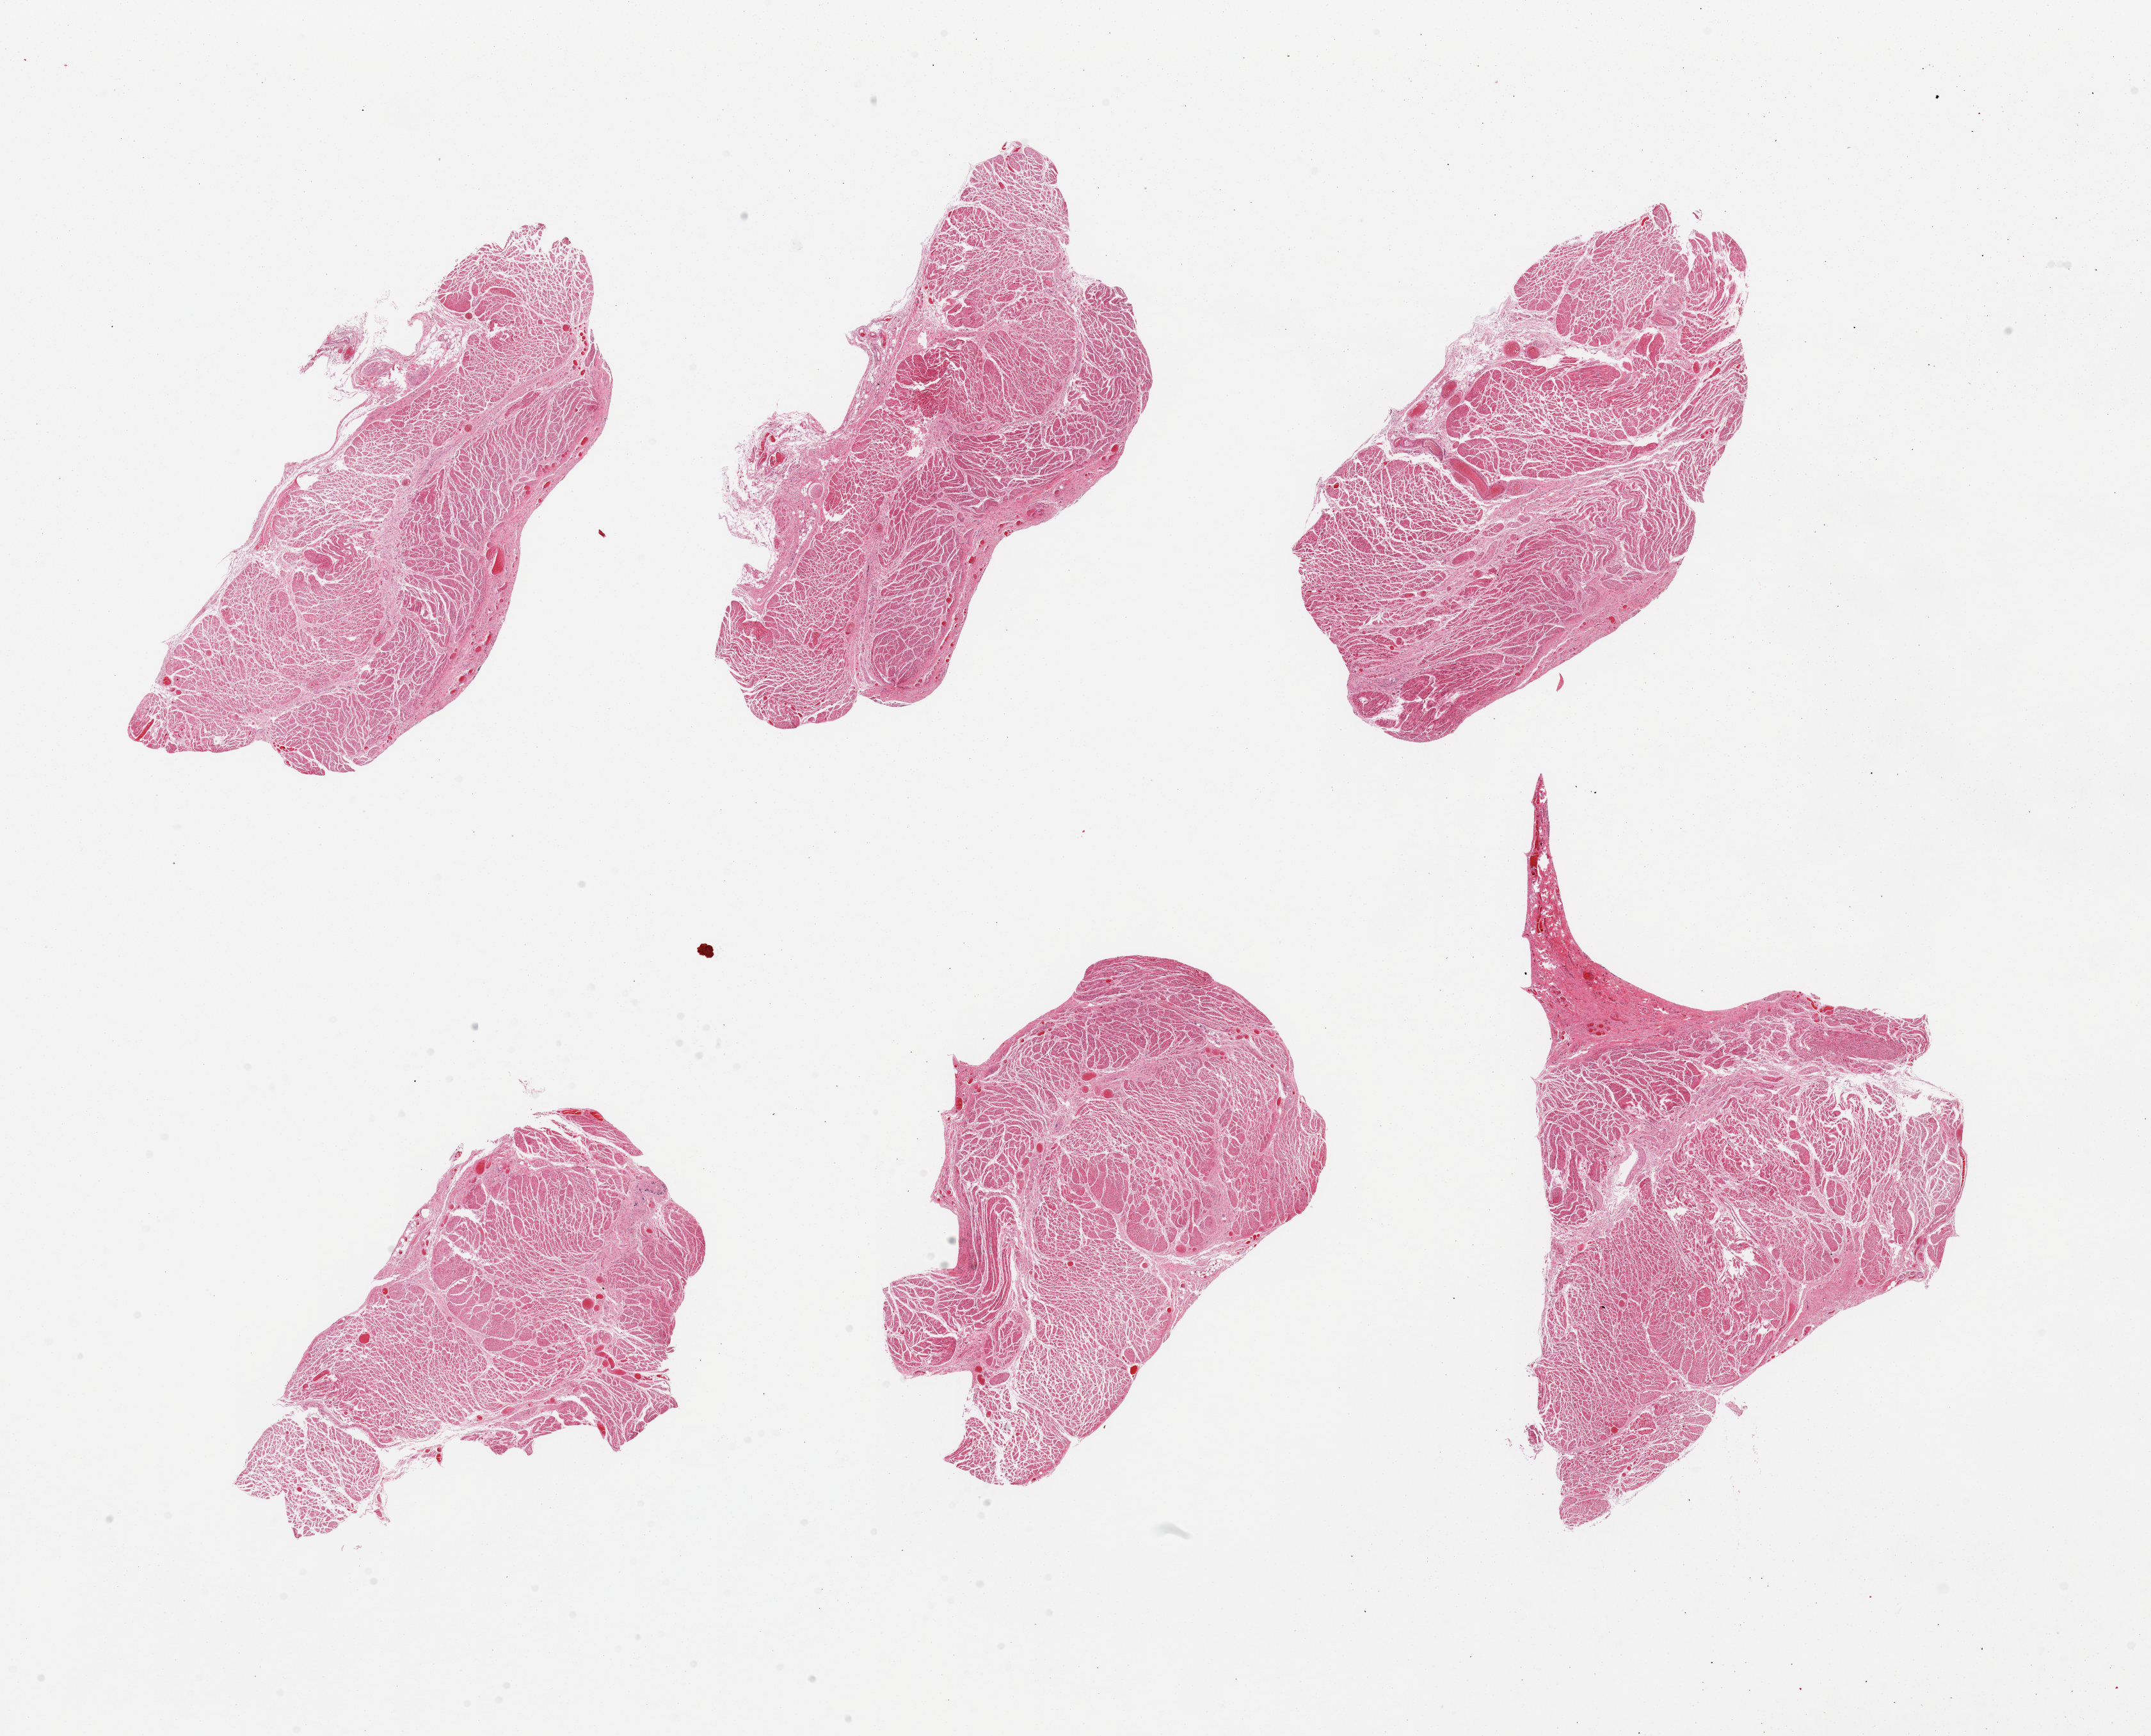
Whole-slide image, H&E stain, brightfield, shown as a low-resolution overview of the whole scanned area (about 26.6 x 21.5 mm). PAXgene-fixed, paraffin-embedded tissue. Section of gastroesophageal junction (target tissue). Donor tissue sample.
Review note (as recorded): 6 pieces, all target muscularis.